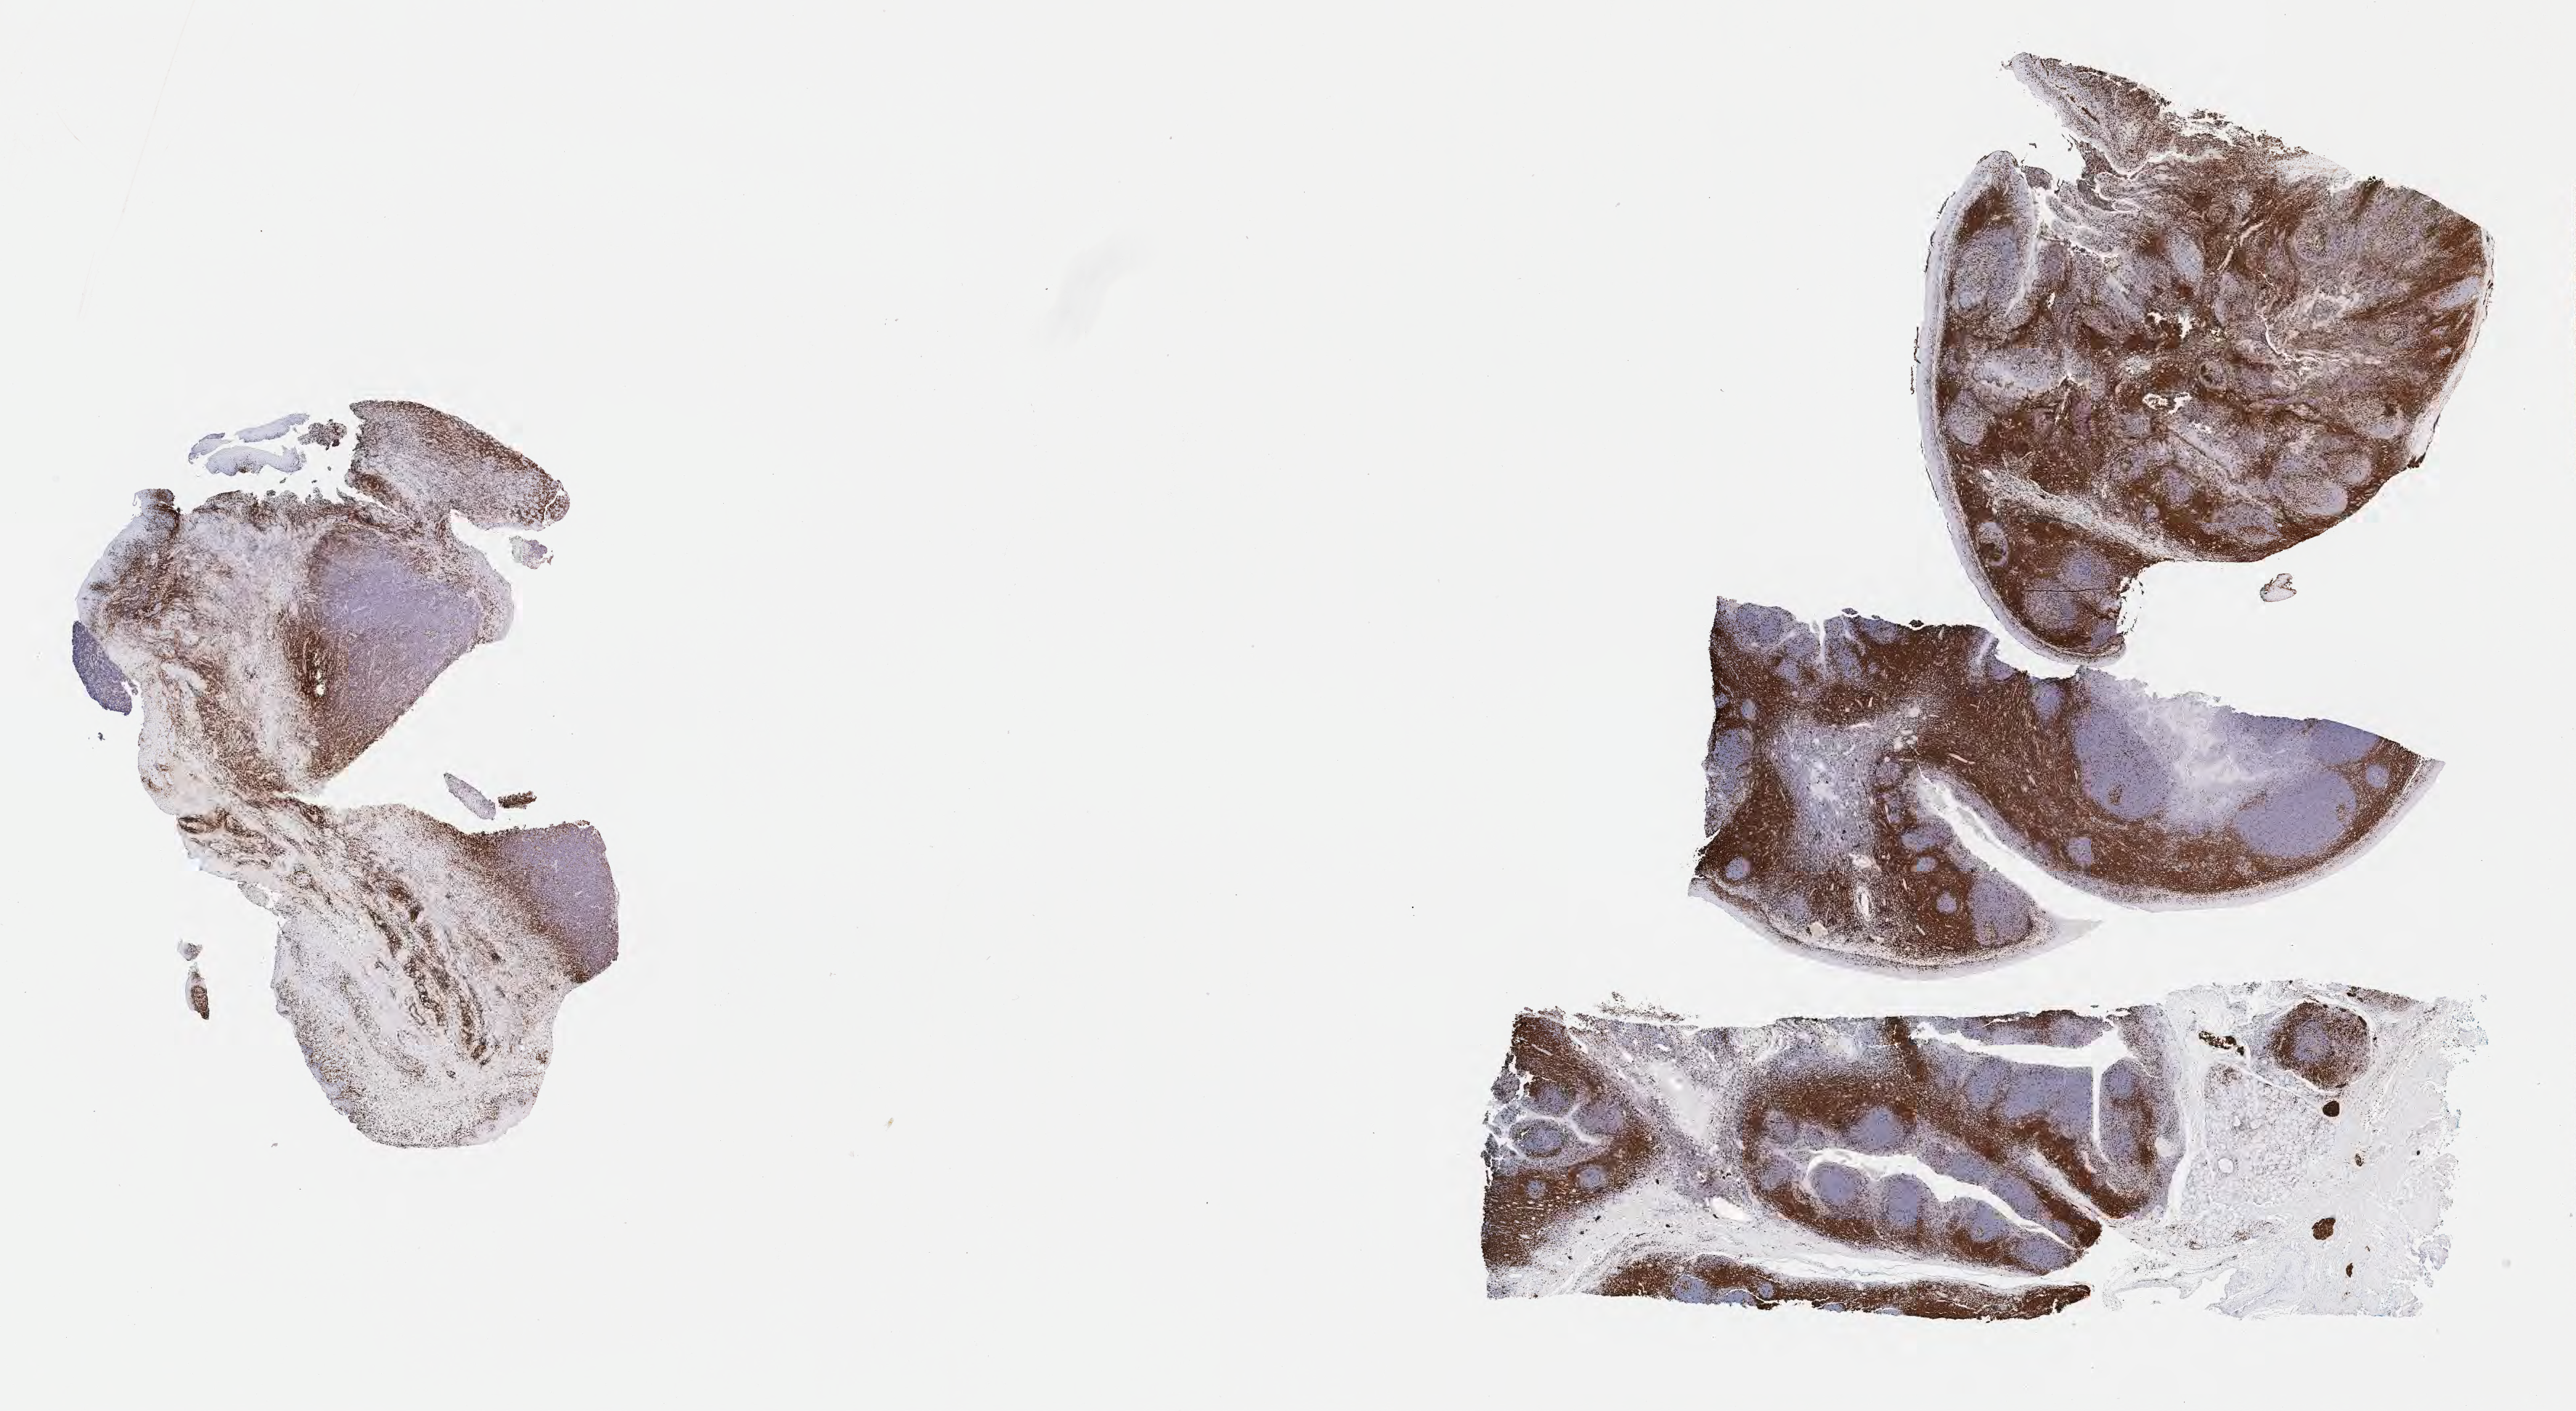
IHC for CD3, whole-slide image — low-resolution overview of the scanned area, about 28.7 x 15.7 mm, specimen: tumor tissue, anatomic site: cranium. Patient male; age 10 years.
* histologic diagnosis: Burkitt lymphoma, NOS